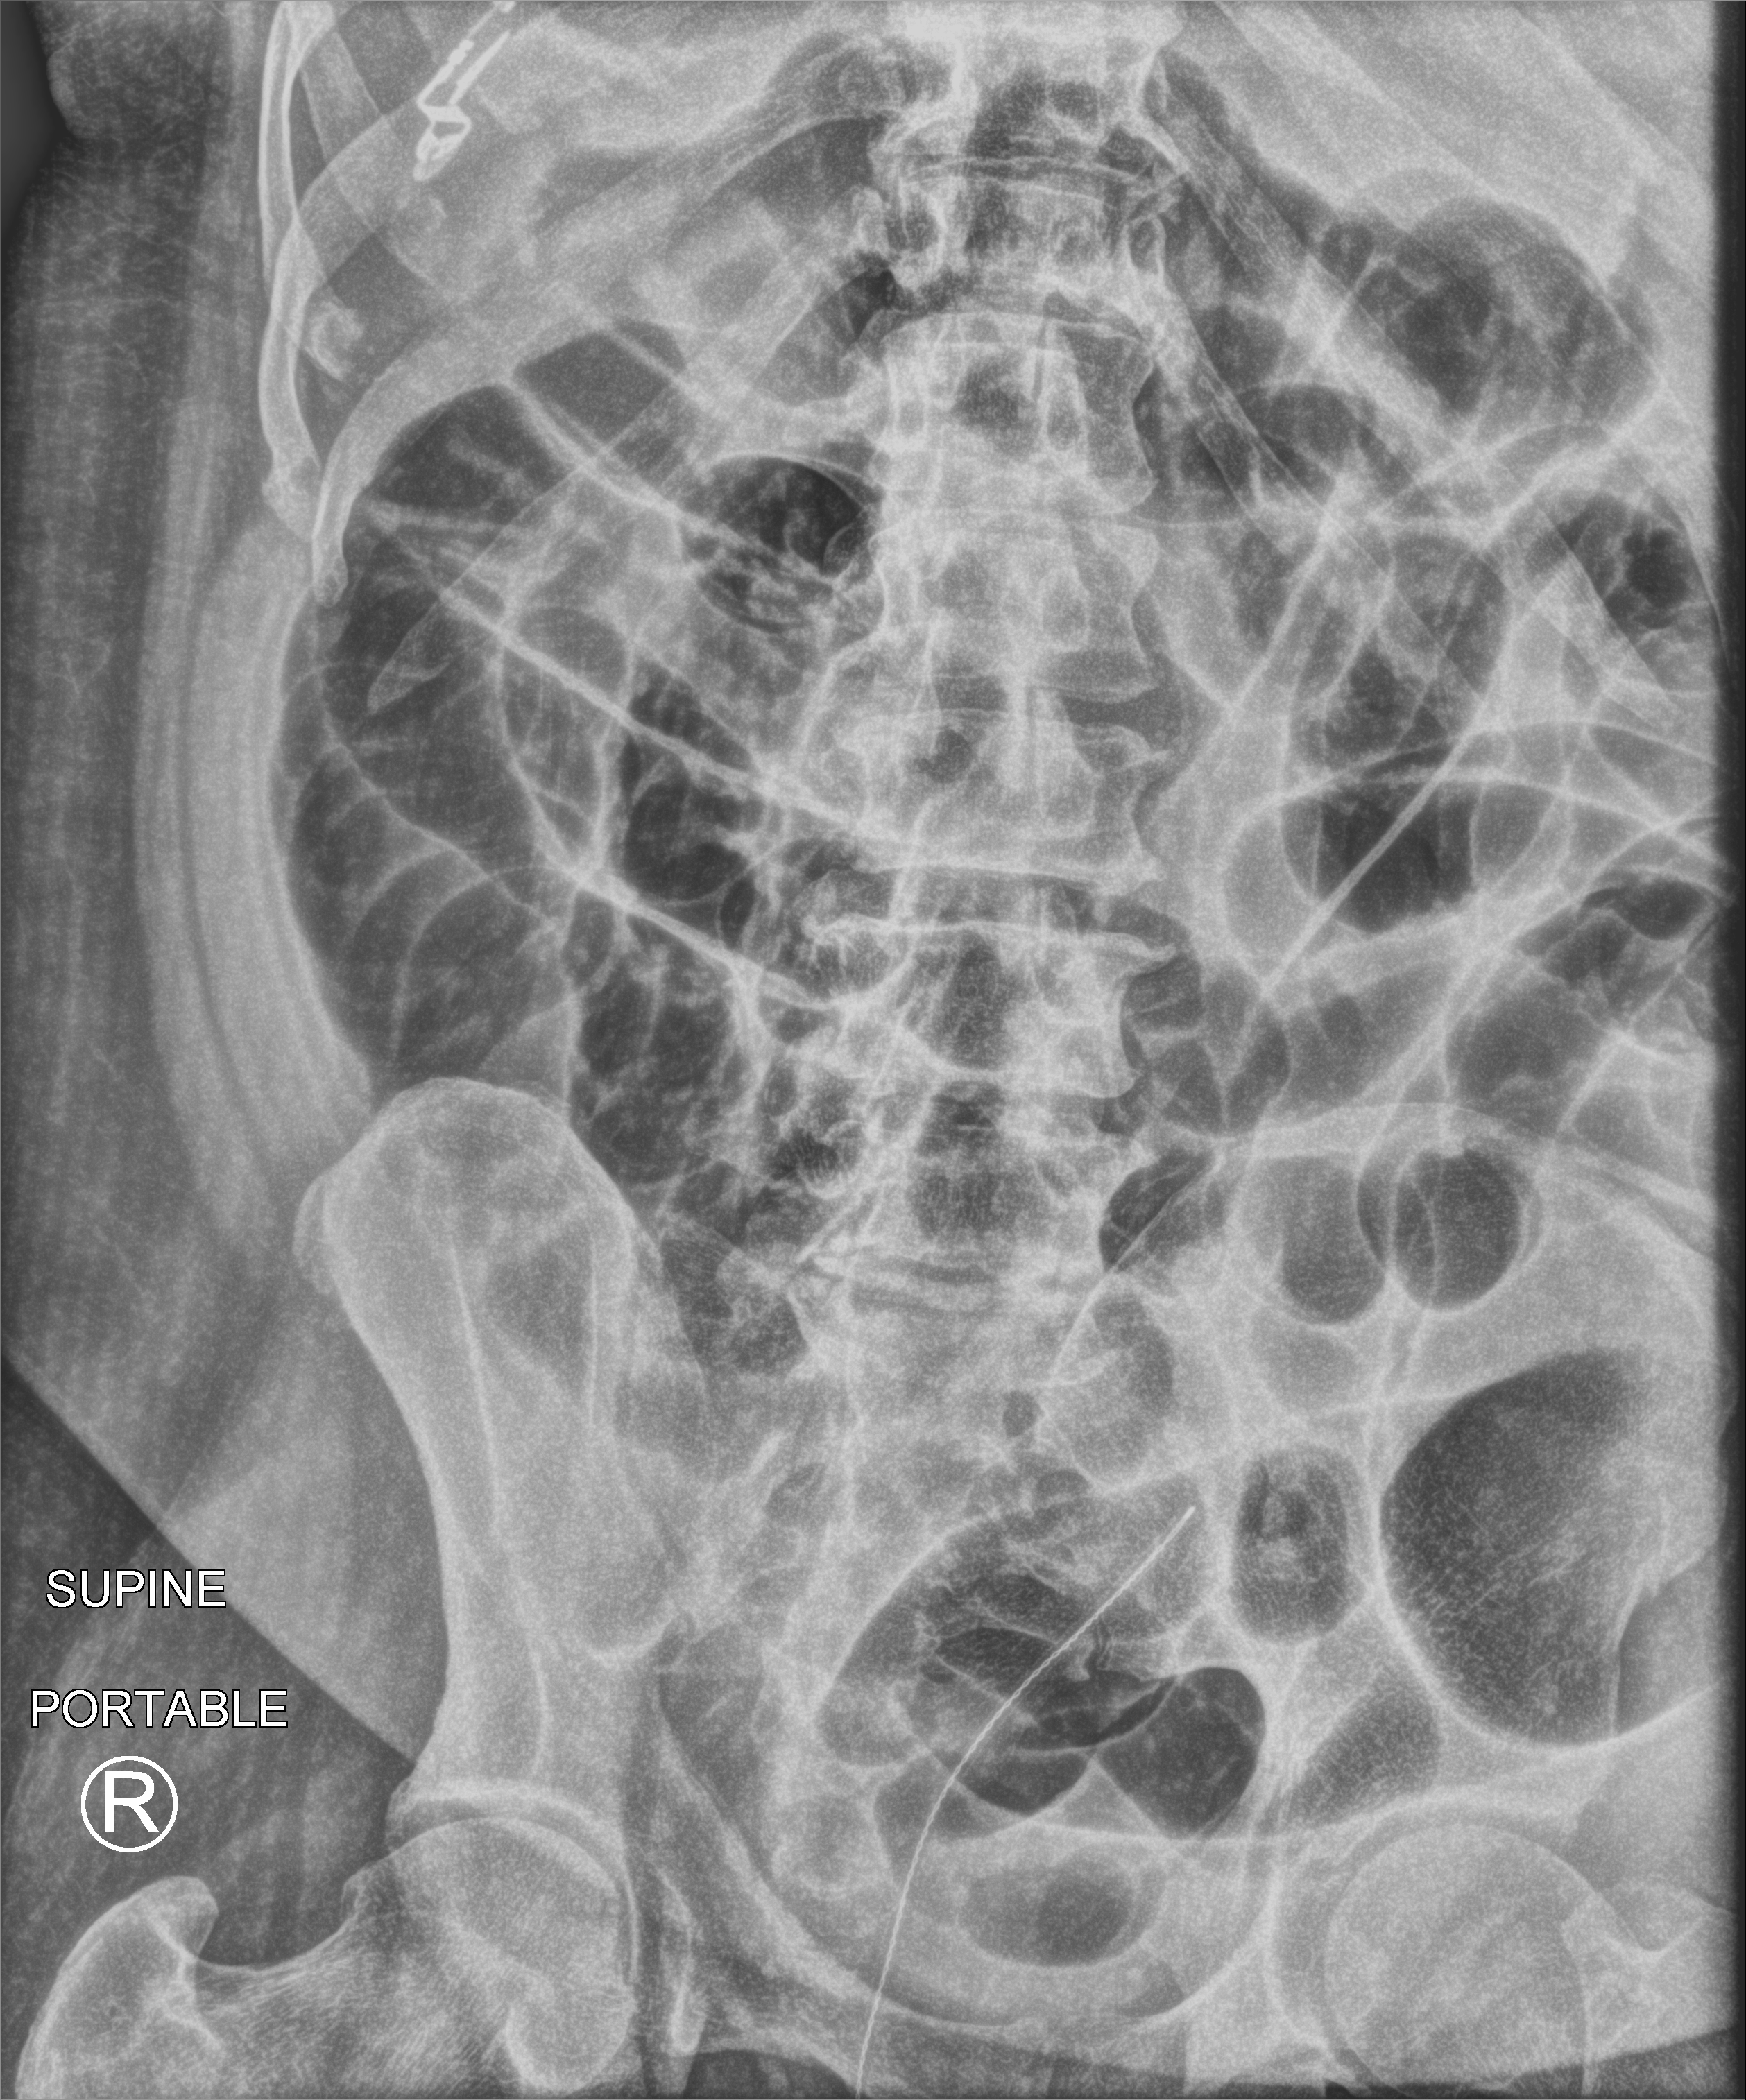
Abdomen X-ray (portable), anteroposterior (AP) projection. Patient hospitalised with COVID-19; male, aged 18–59 years.
Hospital-stay facts (about this admission, not read from this image; timing relative to this image not recorded): mechanically ventilated during this hospital stay: yes; length of hospital stay: 41 days; admitted to intensive care during this hospital stay: yes.